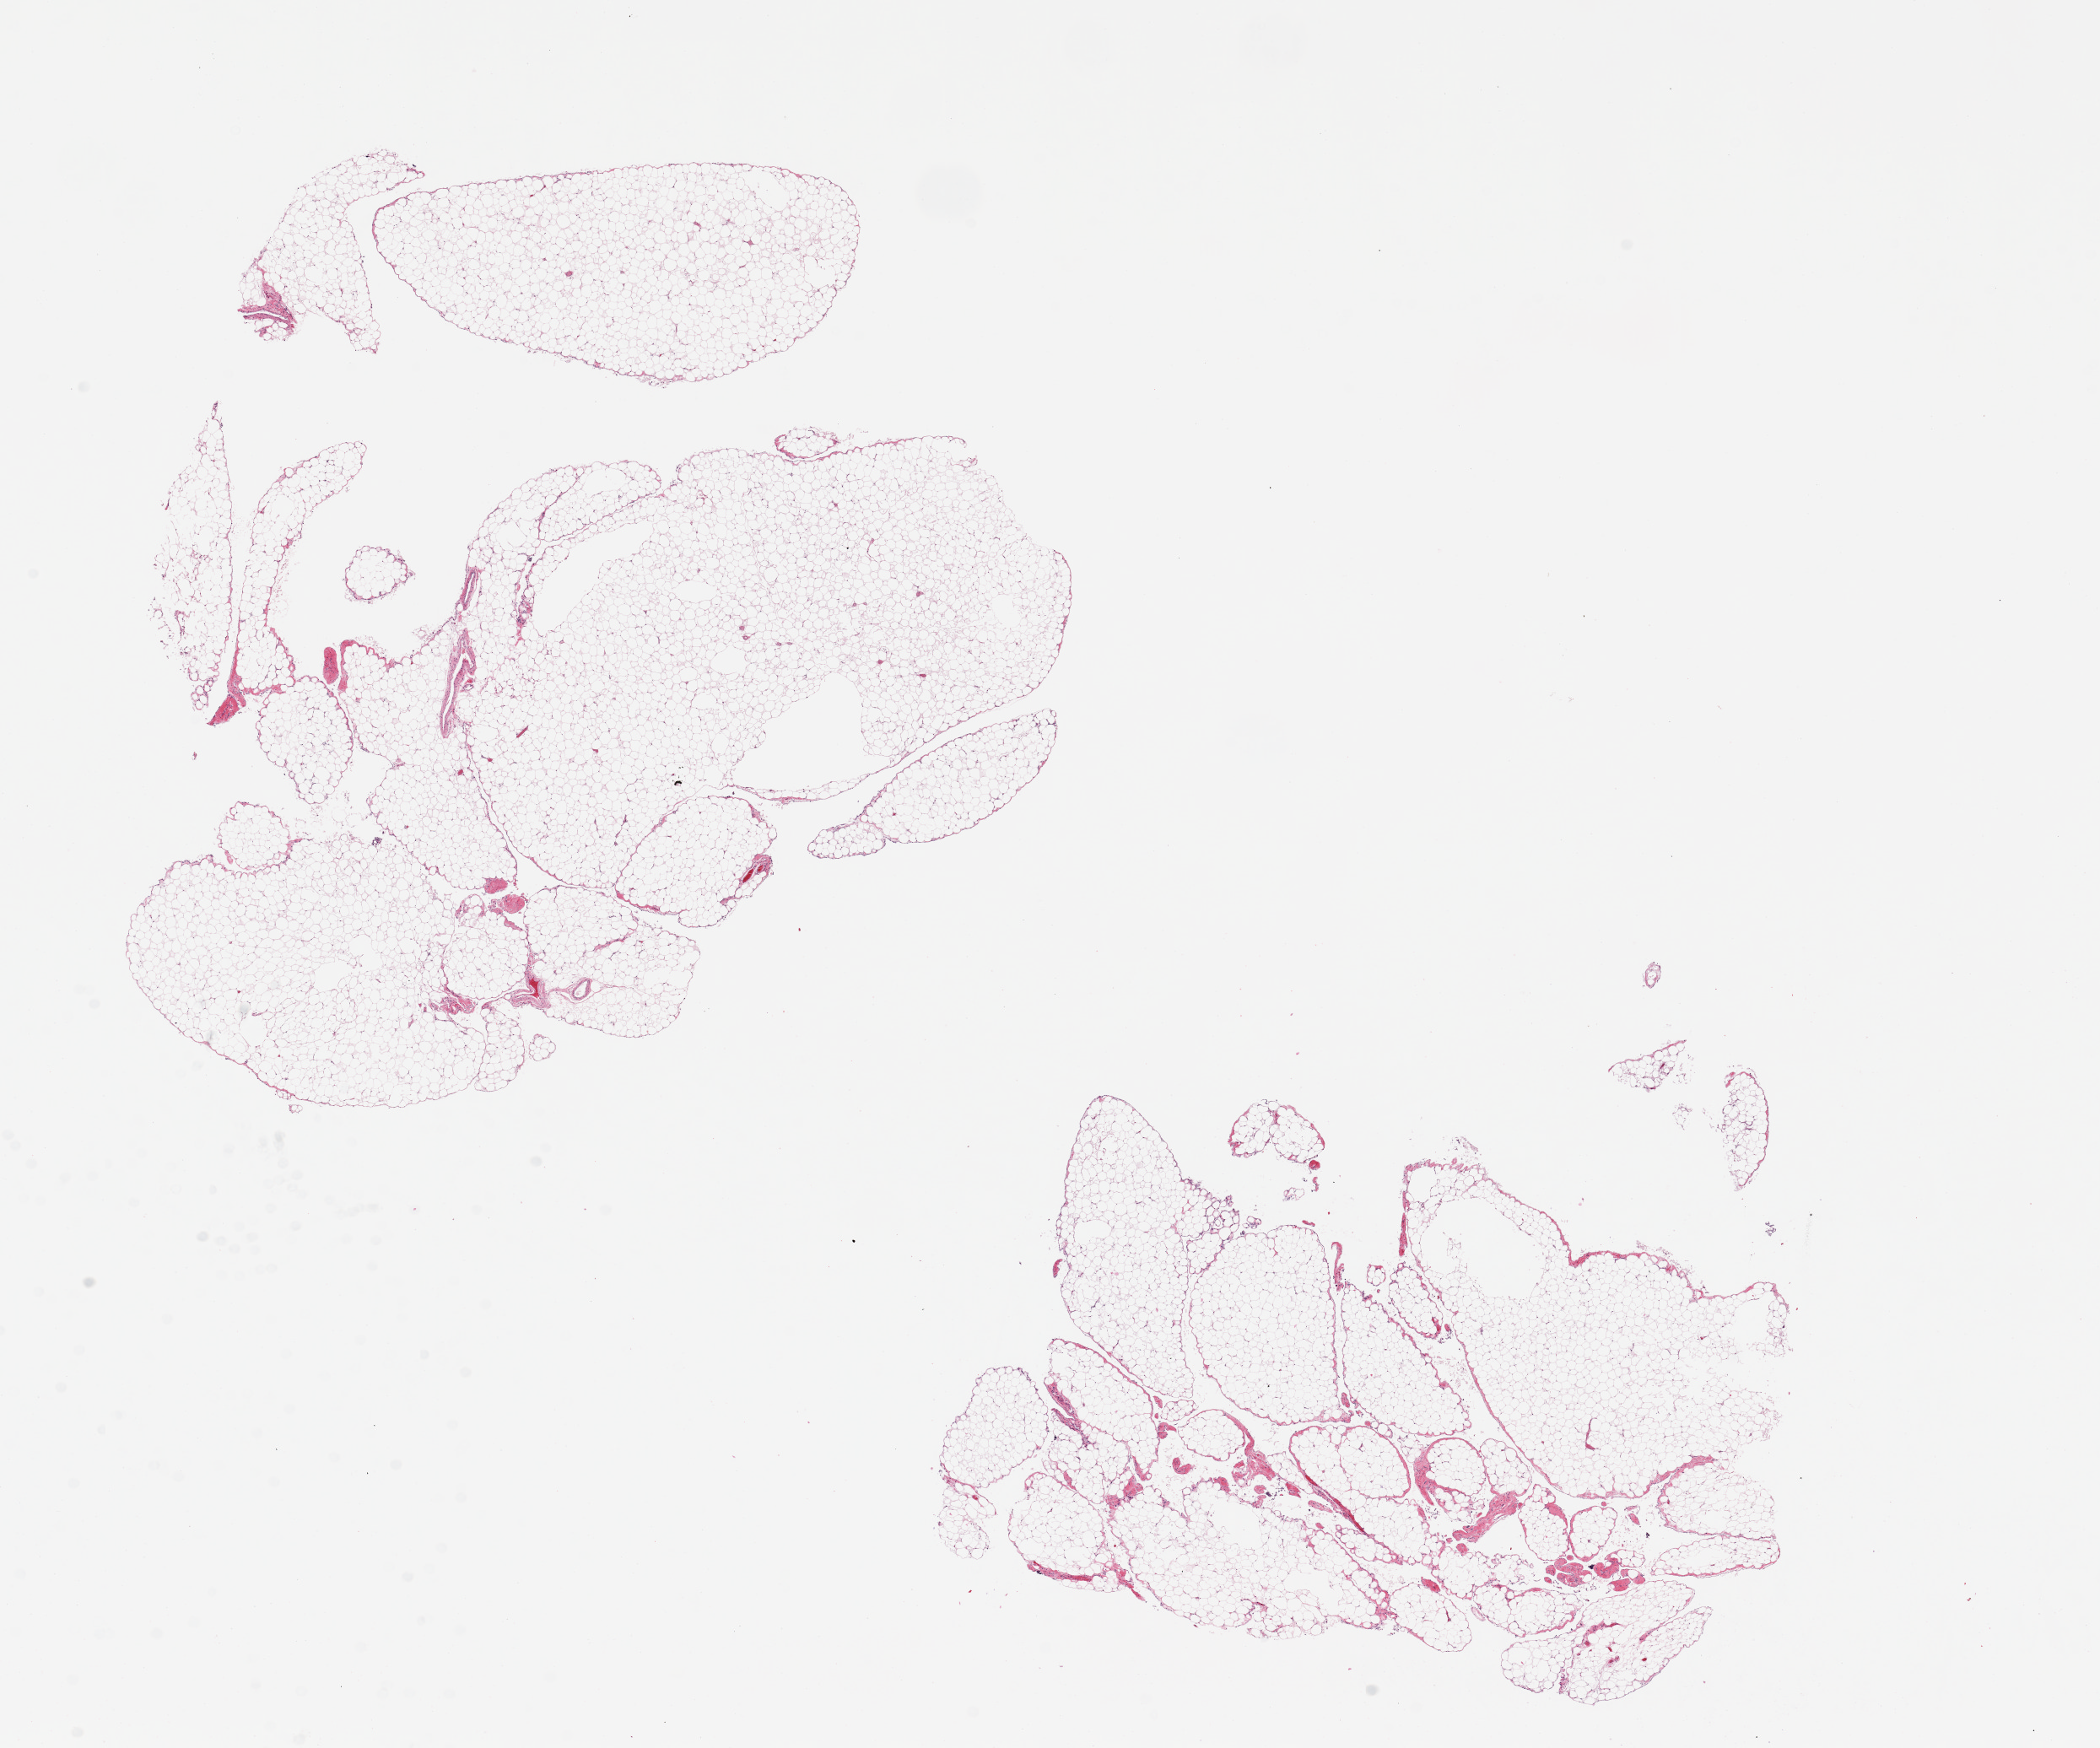
Digitized haematoxylin and eosin-stained section, low-resolution overview of the scanned area, about 19.7 x 16.4 mm. PAXgene-fixed paraffin-embedded (PFPE) section. Target tissue: omentum. Tissue donor sample. Donor sex: female.
Review note (as recorded): 2 pieces, 9.5x7 & 8x5mm.